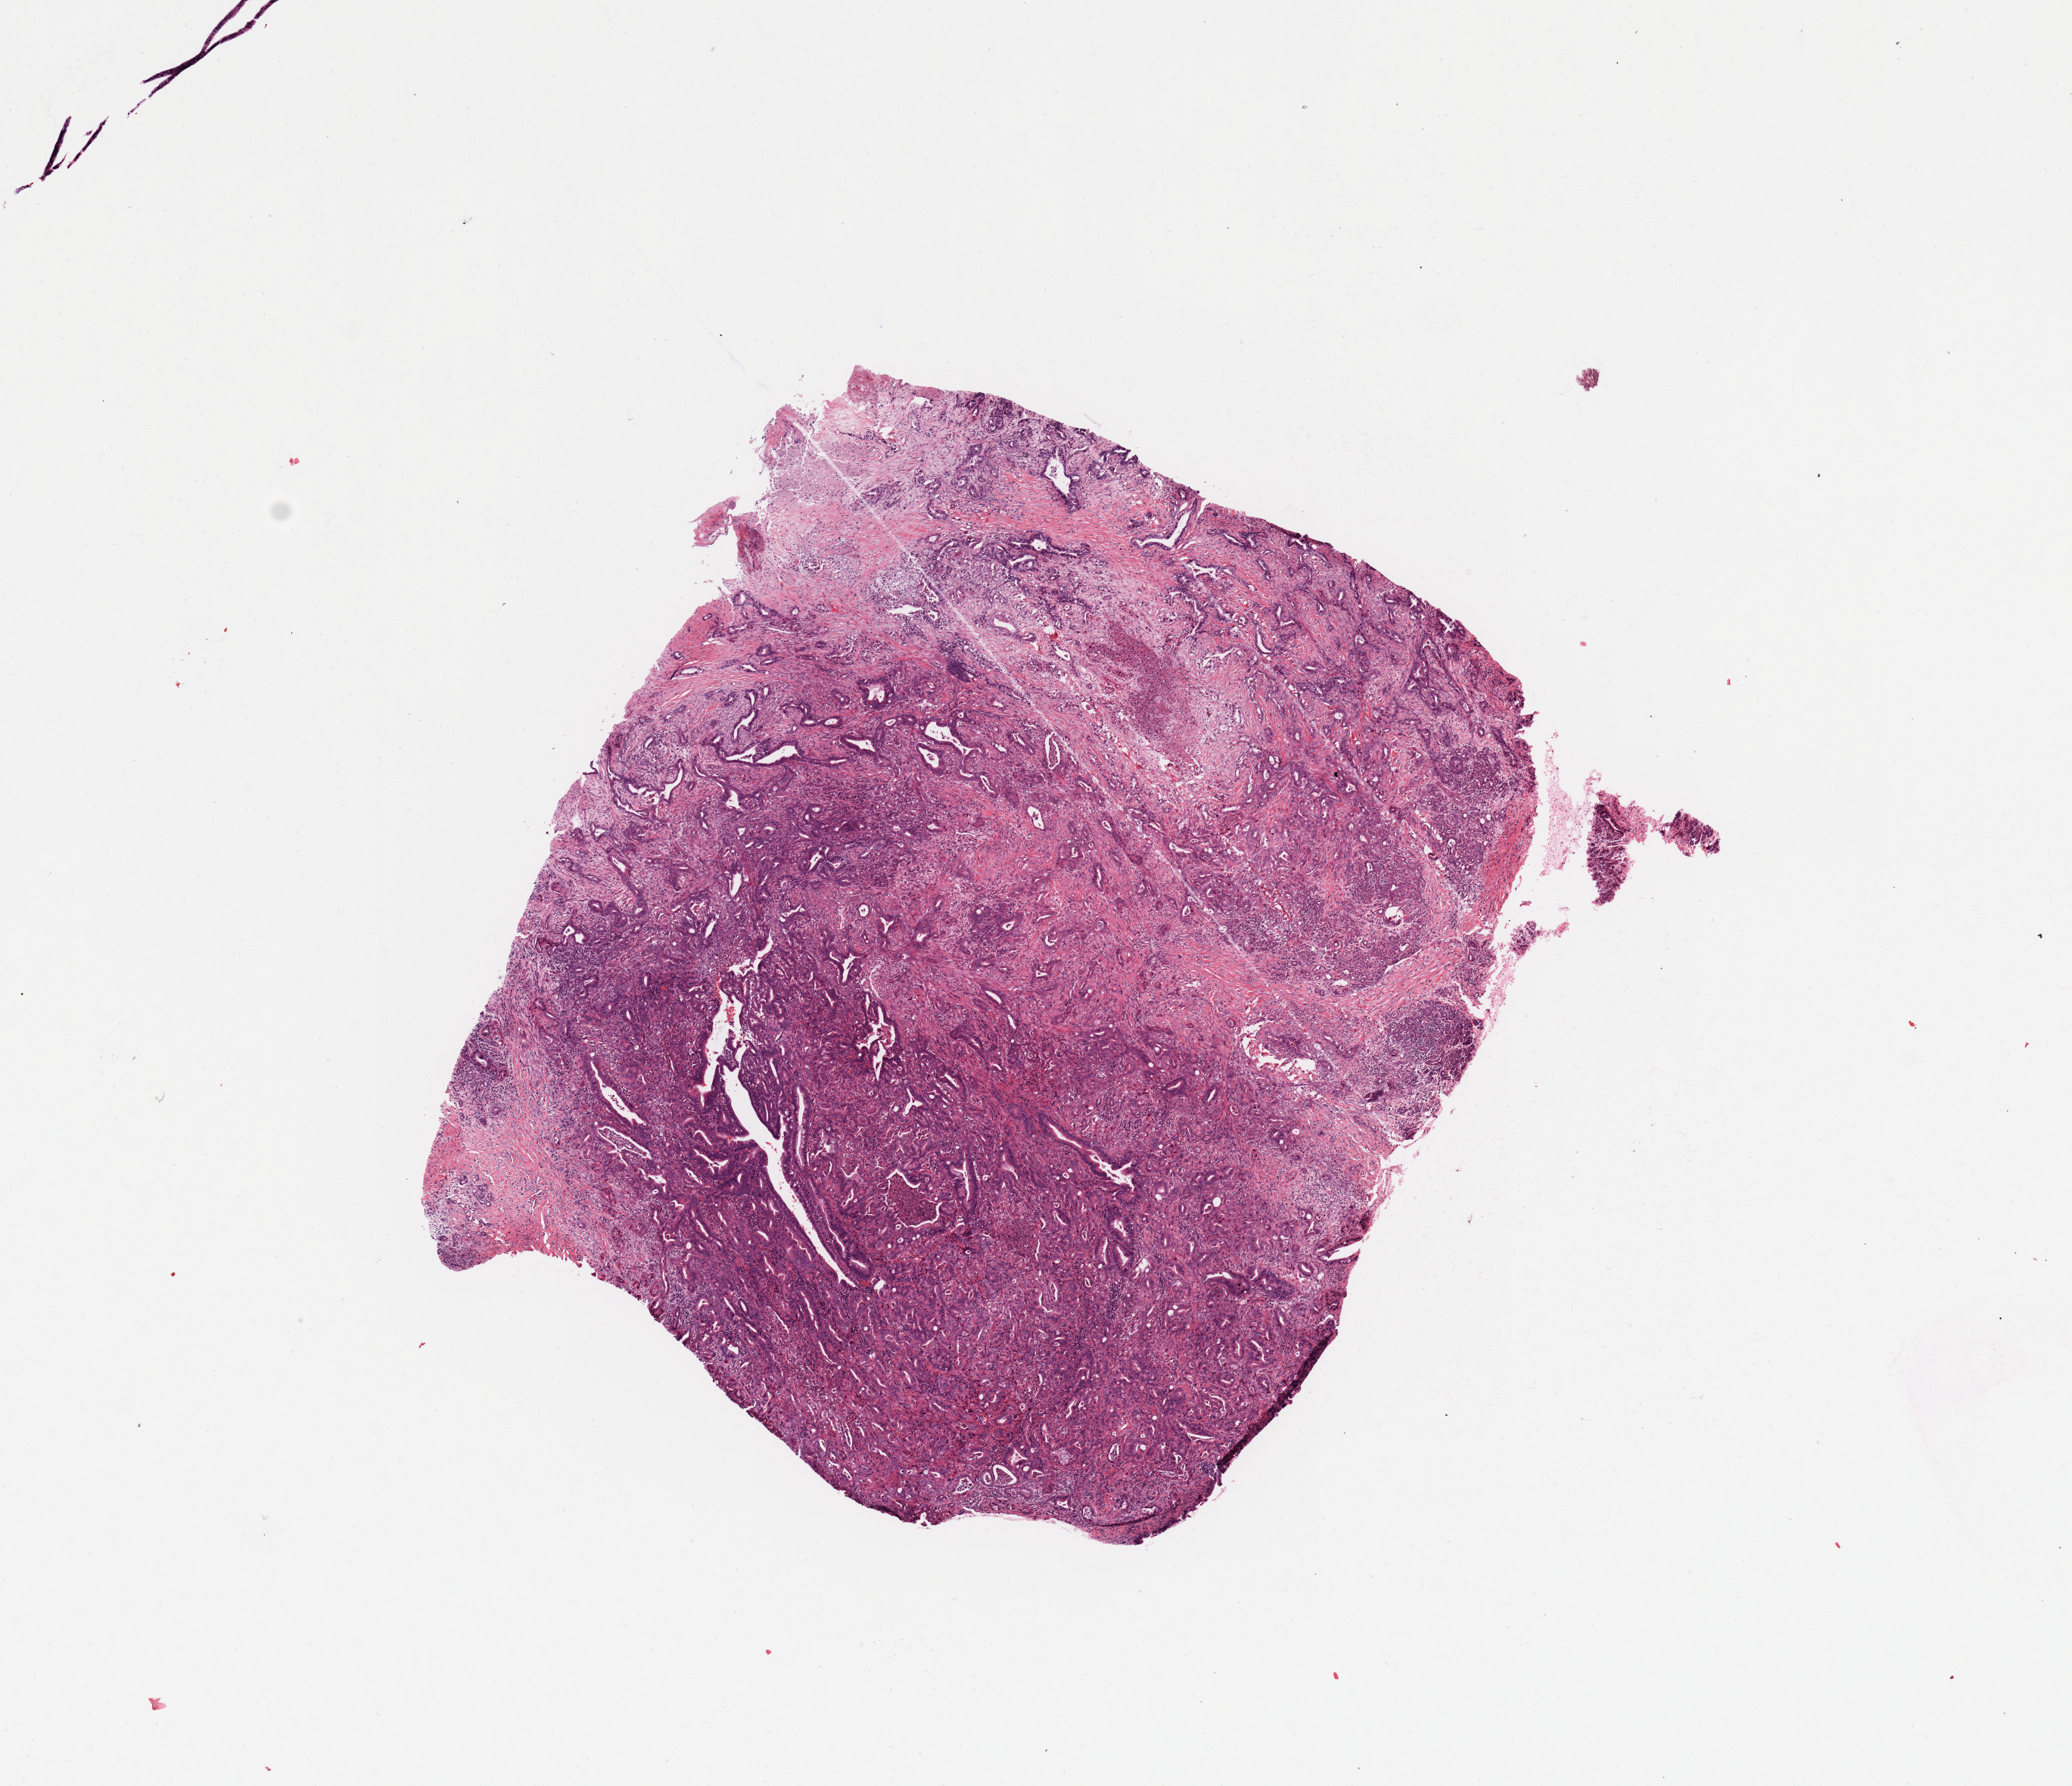
Hematoxylin and eosin (H&E) stained whole-slide image — shown as a low-resolution overview of the whole scanned area (about 10.8 x 9.3 mm, acquisition: 20x scan), tumour tissue sample, sampled site: pancreas. Female, 62 y/o. Histologic grade: G3 (poorly differentiated). Slide review estimates, as recorded: tumour nuclei 80%, necrosis 5%.
Diagnosis: Infiltrating duct carcinoma, NOS. Primary tumour site (as recorded): body. AJCC pathologic stage: IIB.